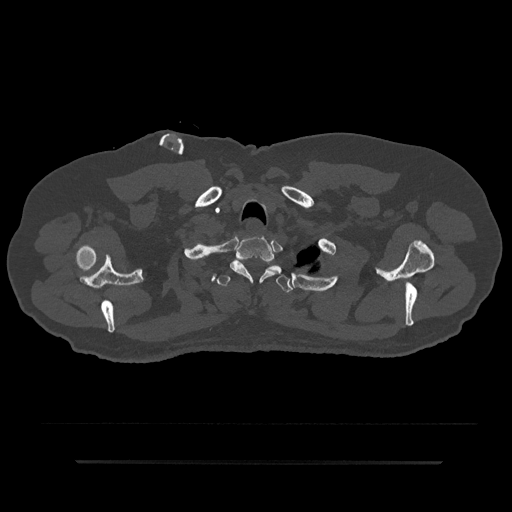
CT including the spine, one axial slice; slice 725 of 797 in the series (ordered by position); 120 kVp; bone window (W 1800 / L 400 HU); 0.5 mm slice thickness; 512 × 512 image matrix, field of view 464 × 464 mm. Male patient, age 59 years. Case-level facts recorded for this patient, not image findings: primary cancer: bile ducts.
Structures marked on this image (semi-automatically segmented with operator editing):
- T1 vertebra: box from (x=230, y=236) to (x=277, y=282) px
- T2 vertebra: (x=216, y=265)–(x=292, y=293)